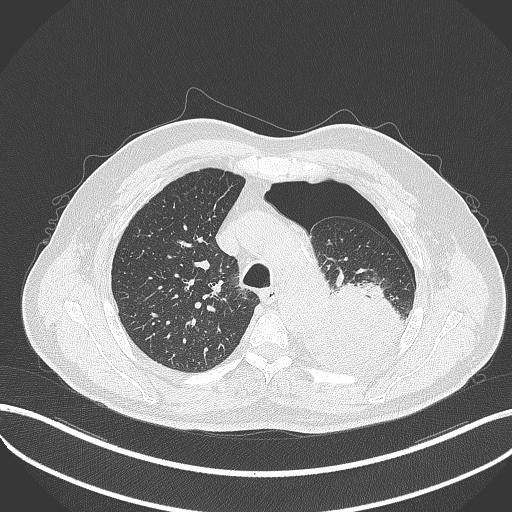
Chest CT, one axial slice. Position 378 of 464 along the scan axis. Reconstruction kernel B70f. Lung window (W 1500 / L -600 HU). 1 mm slice thickness. 512 × 512 image matrix. Male patient, age 76 years. Case-level facts recorded for this patient, not image findings: clinical TNM (as recorded): T3 N0 M1b.
Outlined on this slice (bounding box drawn by a radiologist):
- lung tumour (recorded histology: adenocarcinoma): bounding box (x1, y1, x2, y2) in pixels: (294, 274, 405, 375)